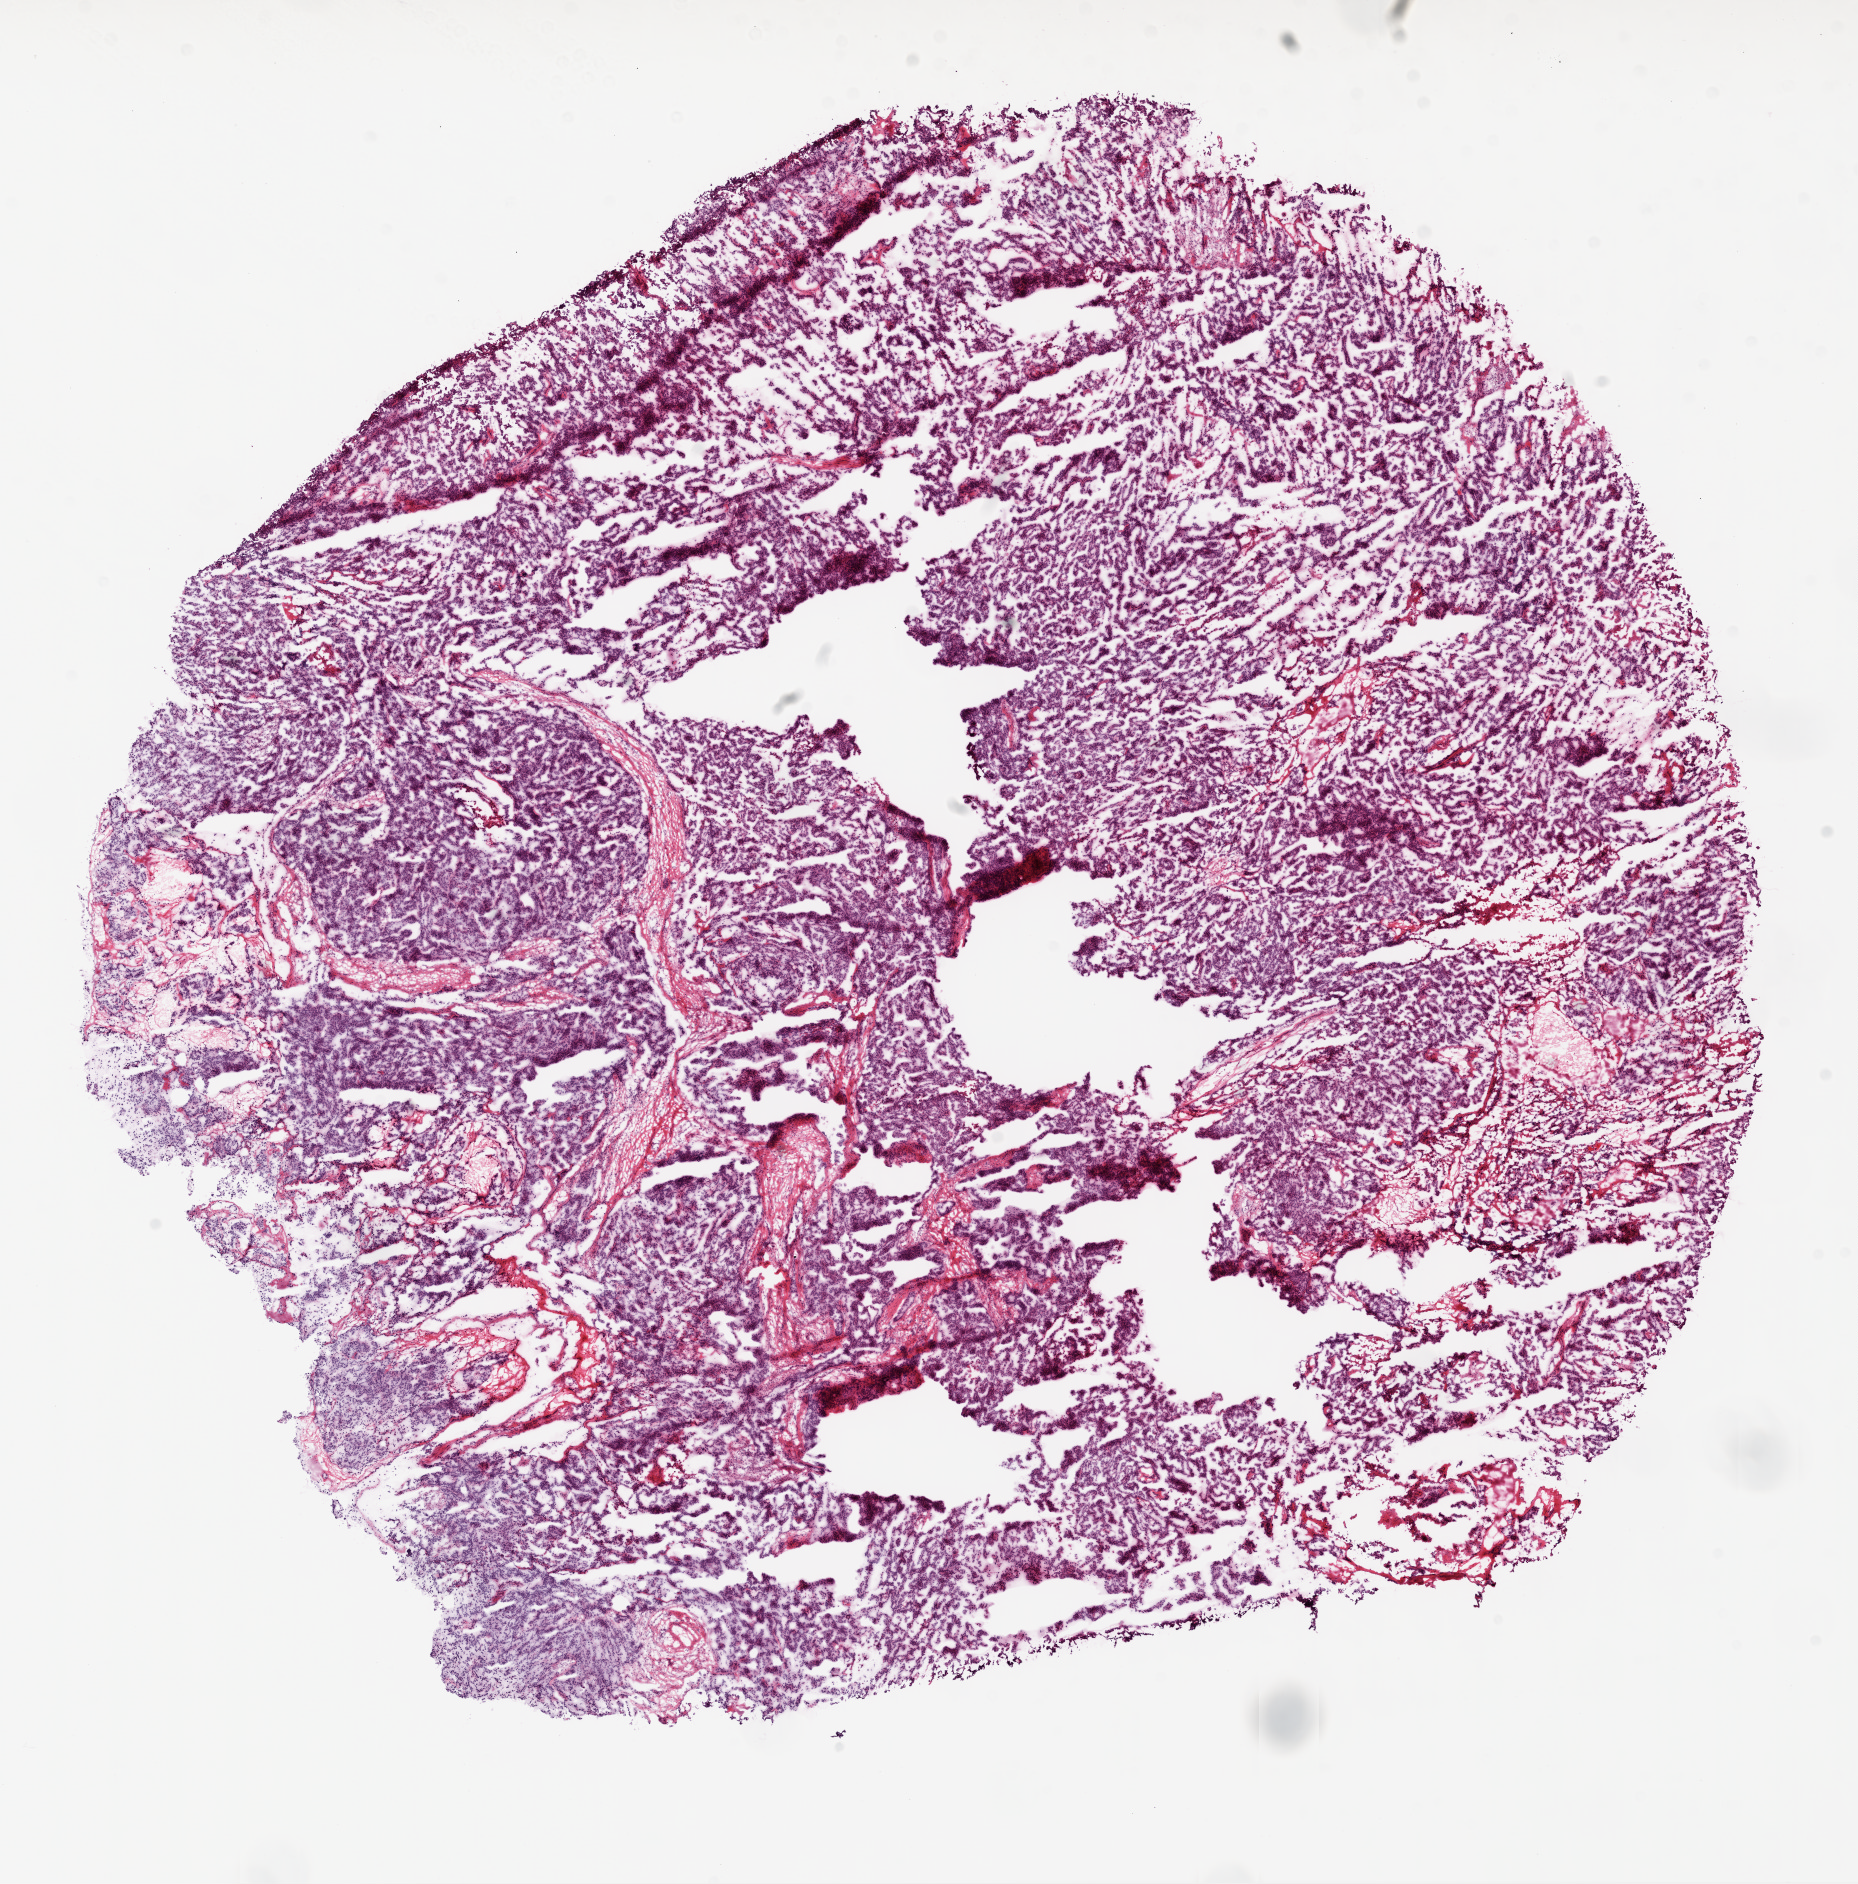
Whole-slide histology image, H&E-stained, a low-resolution overview of the entire scanned area, about 15.0 x 15.2 mm. Frozen section. Ovary, primary tumour sample. Female patient; age at initial diagnosis 54 years. Histologic grade: G3 (poorly differentiated). Slide review estimates, as recorded: tumour cells 85%, tumour nuclei 90%, normal cells 10%, necrosis 5%.
* FIGO stage: IIIC
* pathologic diagnosis: Serous cystadenocarcinoma, NOS